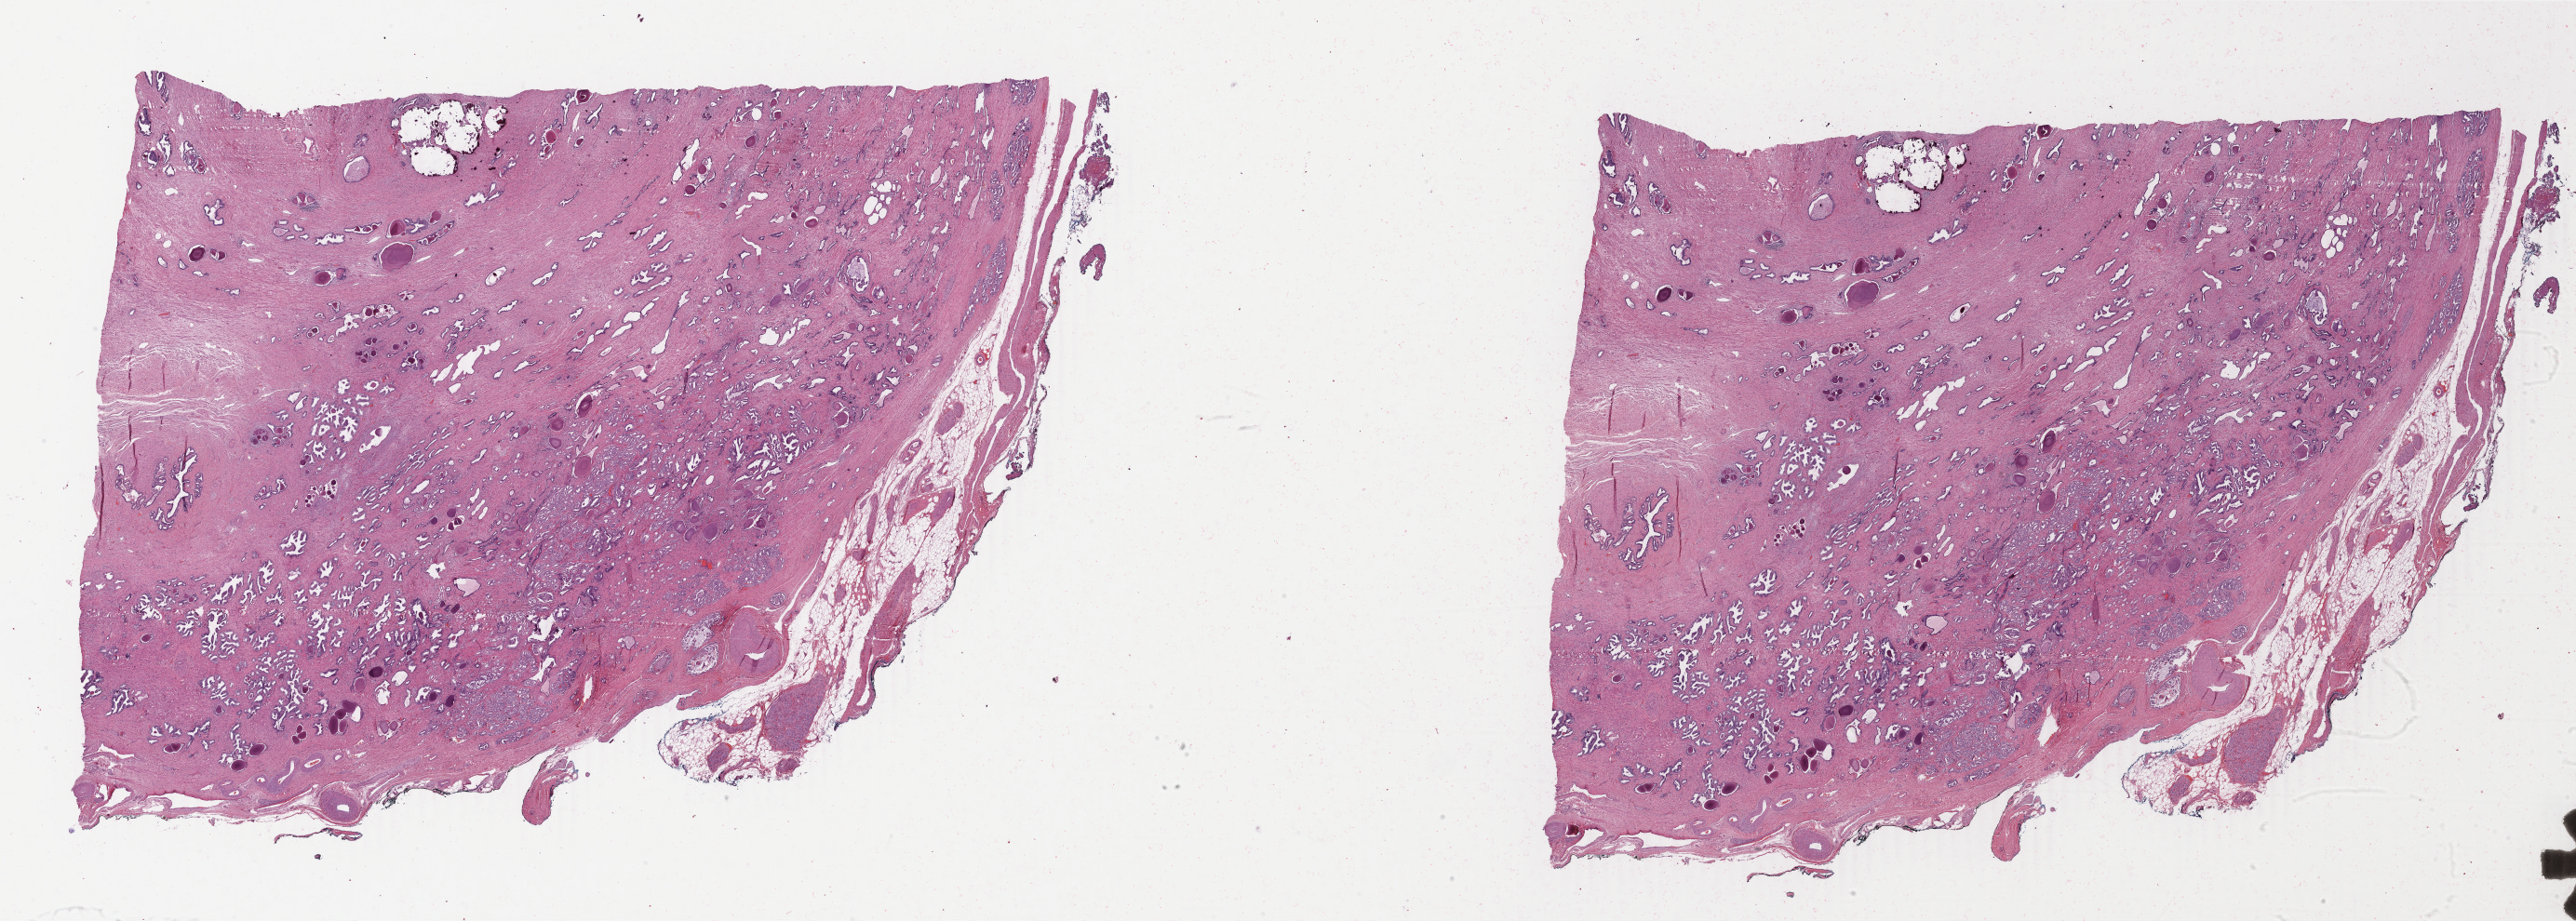
Hematoxylin and eosin (H&E) stained whole-slide image — low-resolution overview of the scanned area, about 44.0 x 15.7 mm; FFPE section; primary tumour sample from the prostate. Male, age 61 years at initial diagnosis.
Pathologic diagnosis: Adenocarcinoma, NOS (prostate gland).